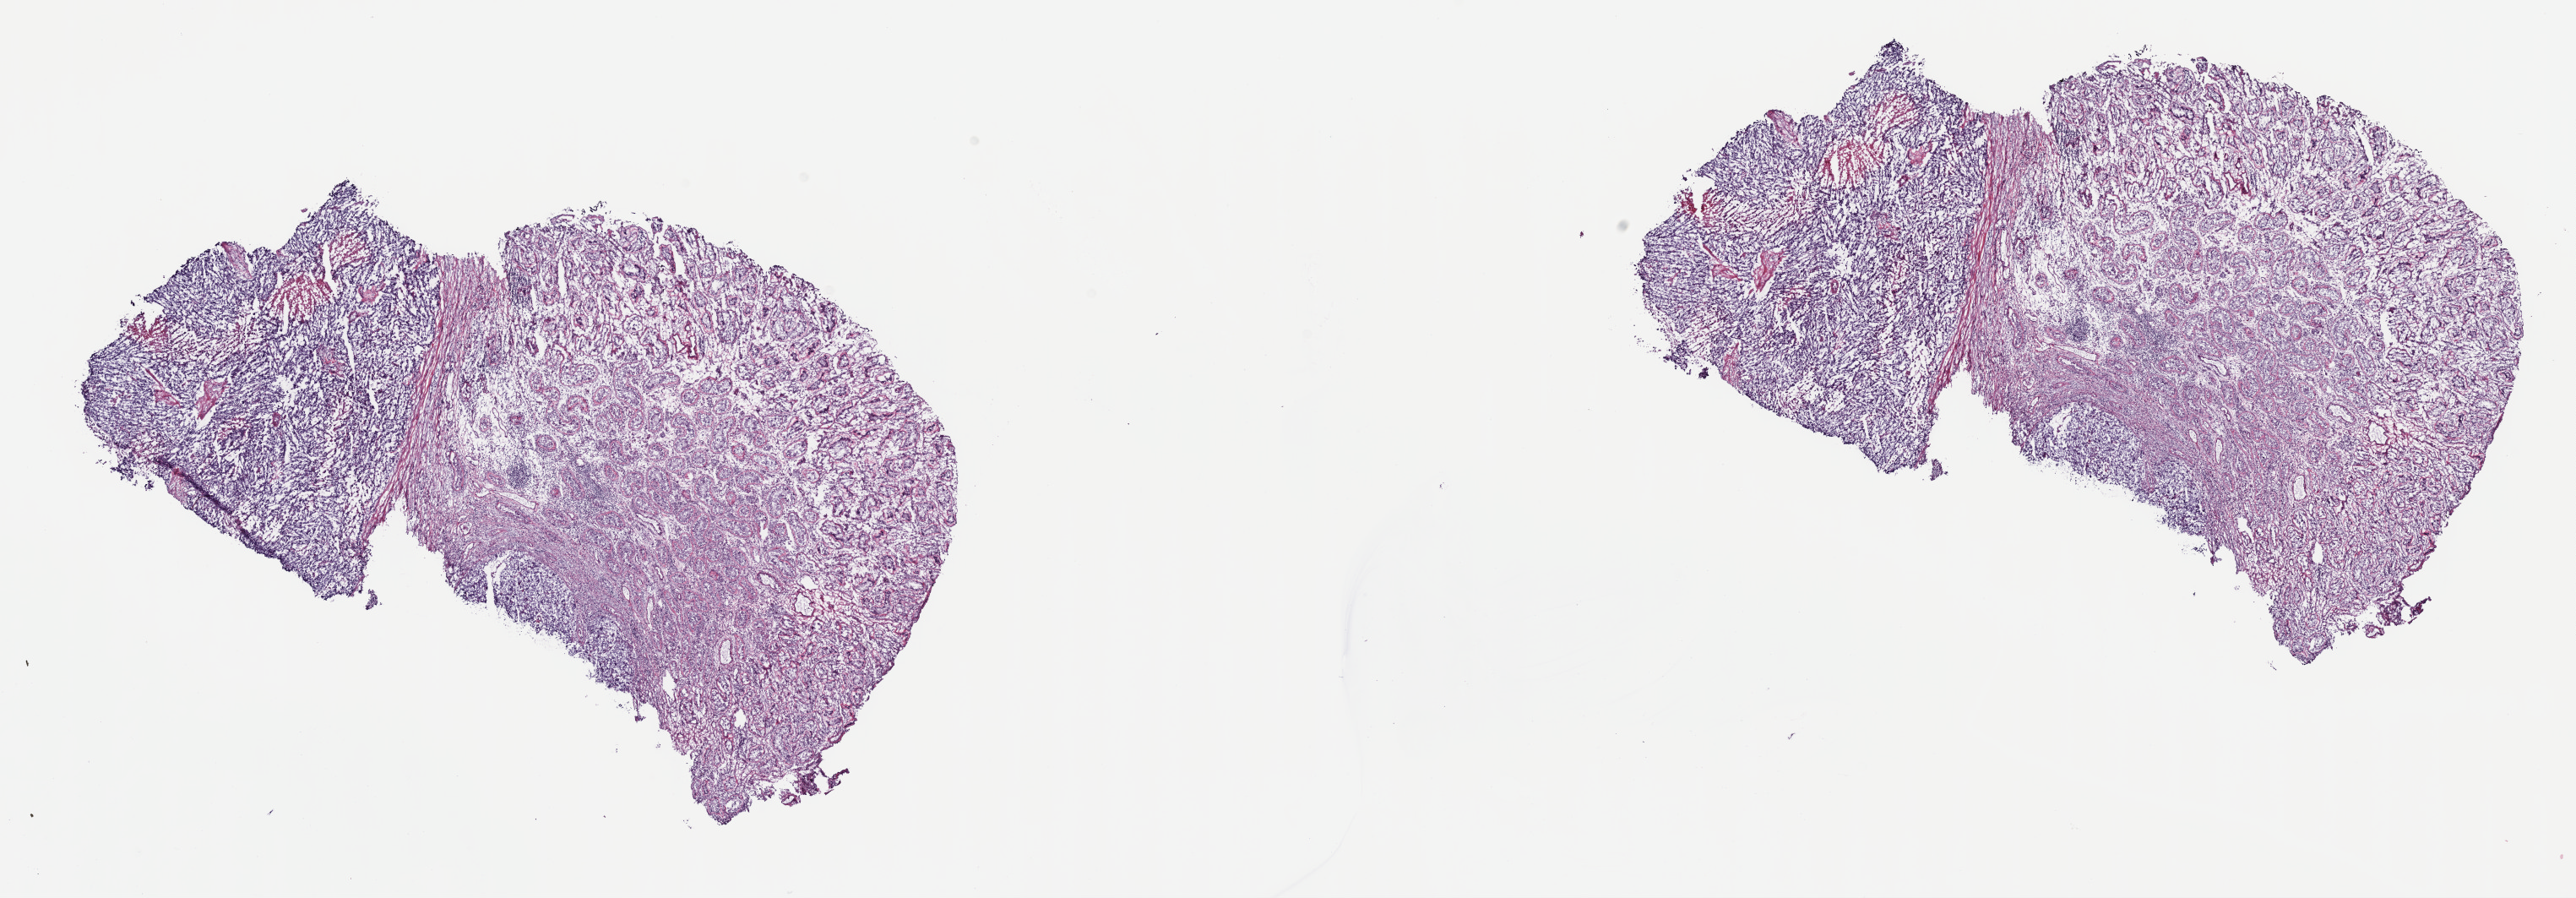
Digitized H&E tissue section (whole slide) — whole scanned area (about 24.7 x 8.6 mm) shown as a low-resolution overview; frozen section from the top of the tissue portion; testis, primary tumour sample. Male, age 33 years at initial diagnosis. Composition of this section per pathologist review: tumour cells 35%, tumour nuclei 40%, normal cells 63%, stromal cells 0%, necrosis 2%. Inflammatory infiltration, as recorded: lymphocyte infiltration 0%, monocyte infiltration 0%, neutrophil infiltration 0%.
Laterality: left. TNM: T1 N1 M0. Pathologic diagnosis: Embryonal carcinoma, NOS. AJCC pathologic stage: IIA (7th edition).